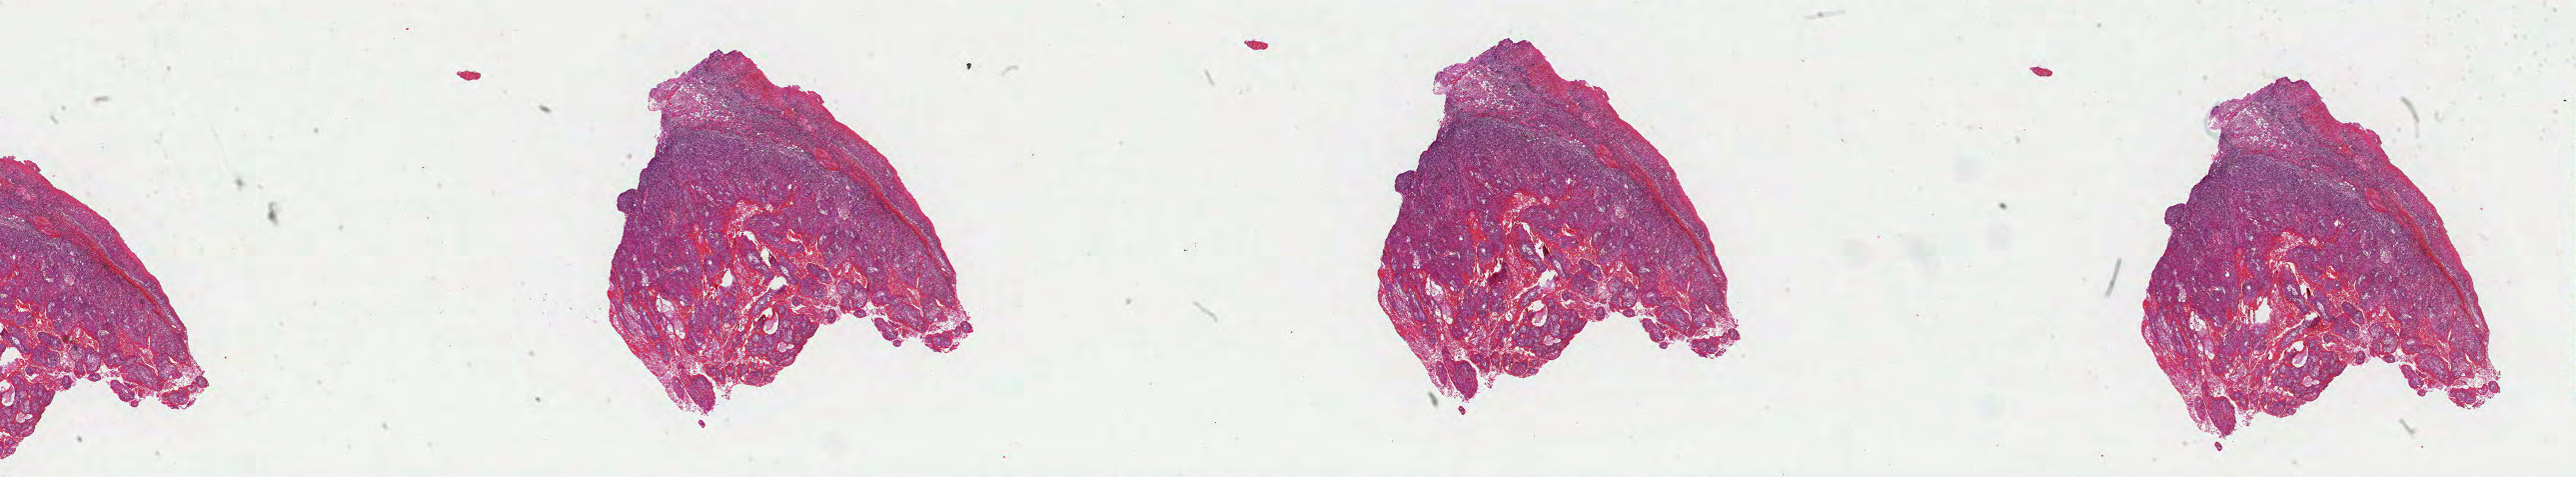
Whole-slide histology image, Hematoxylin and eosin (H&E) stained, low-resolution overview of the scanned area, about 41.8 x 7.7 mm (from a 40x scan); formalin-fixed paraffin-embedded (FFPE) diagnostic section; sample: primary tumour, head and neck. Female, age 77 years at initial diagnosis. Histologic grade: G2 (moderately differentiated).
Pathologic diagnosis: Squamous cell carcinoma, NOS (tongue, NOS). TNM: T1 N0. AJCC pathologic stage: I (7th edition).